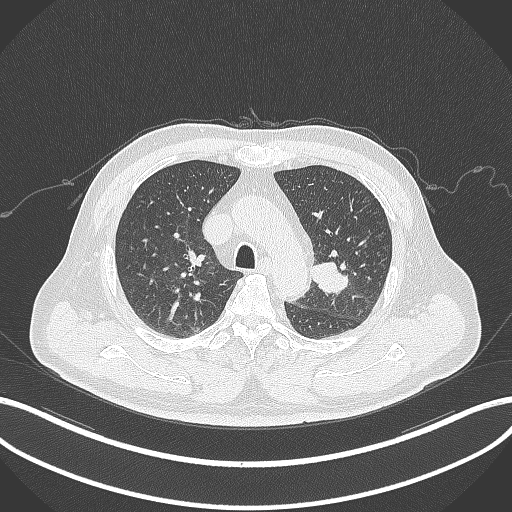
Chest CT, one axial slice; position 219 of 286 along the scan axis; reconstruction kernel B70f; 120 kVp; lung window (W 1500 / L -600 HU); 1 mm slice thickness; 512 × 512 image matrix. Male patient, age 67 years. Case-level facts recorded for this patient, not image findings: clinical TNM (as recorded): T2a N1 M0; histopathological grade: G3.
Annotated regions visible in this slice (rectangle marked by the reading radiologist):
- lung tumour (recorded histology: adenocarcinoma): box from (x=309, y=259) to (x=351, y=297) px